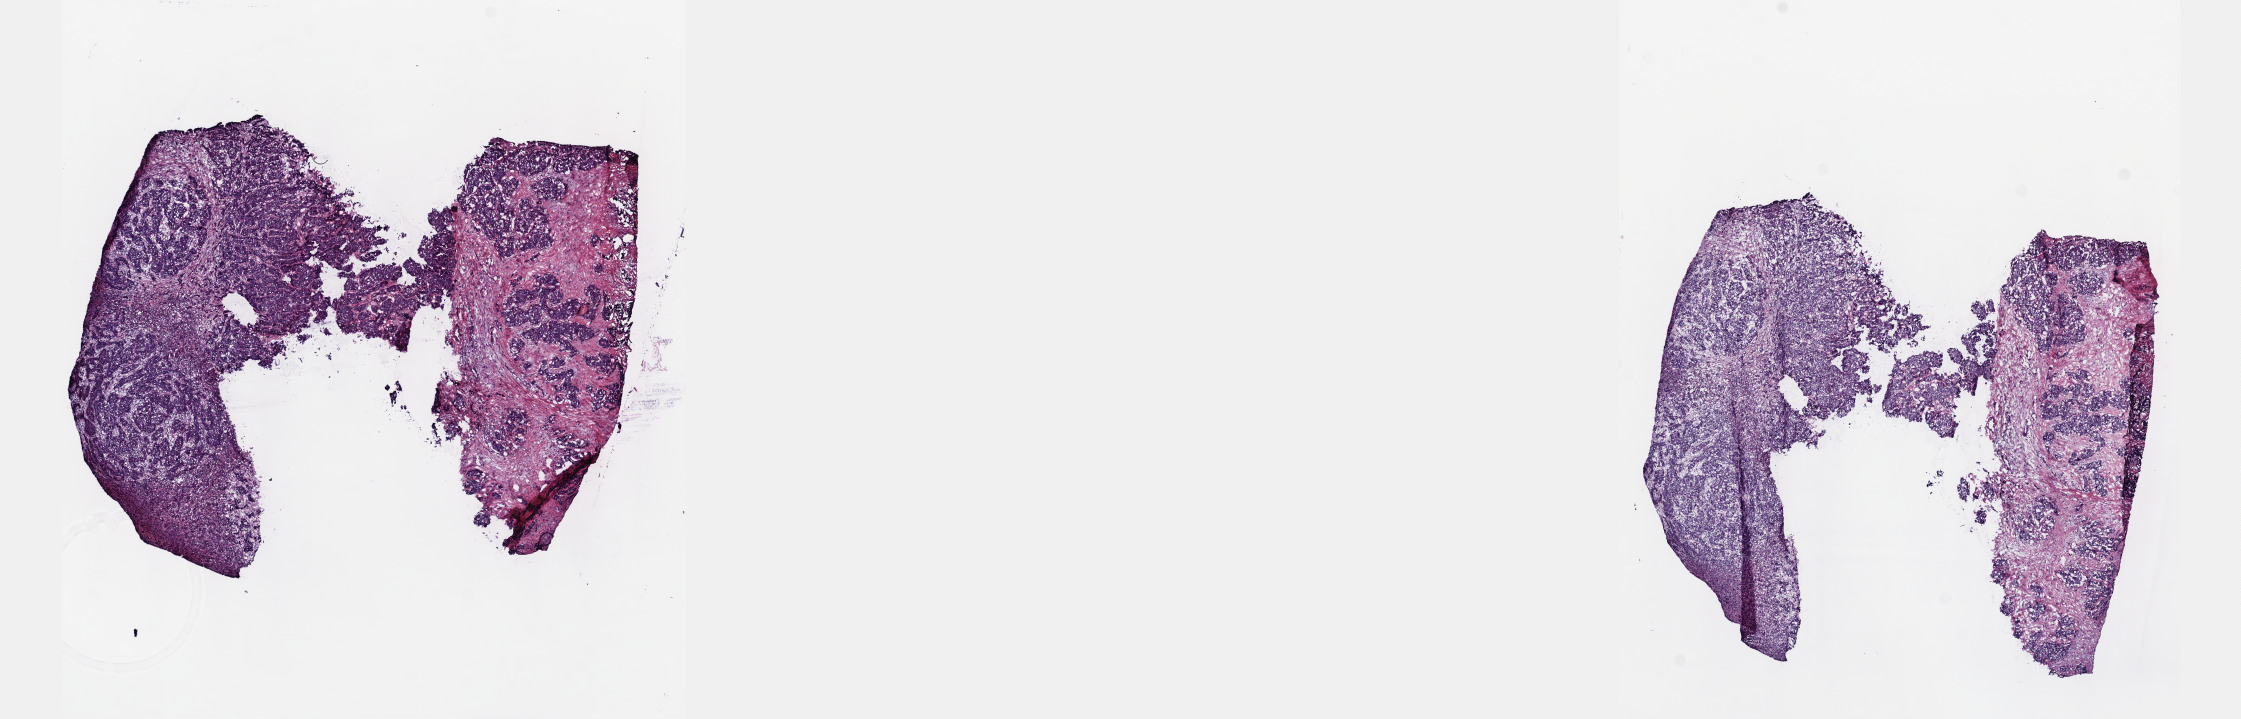
Hematoxylin and eosin (H&E) stained whole-slide image — low-resolution overview of the scanned area, about 18.1 x 5.8 mm, frozen section from the top of the tissue portion, liver, primary tumour sample. Female patient; age at initial diagnosis 45 years. Slide review estimates, as recorded: tumour cells 37%, tumour nuclei 80%.
Pathologic diagnosis: Hepatocellular carcinoma, NOS.